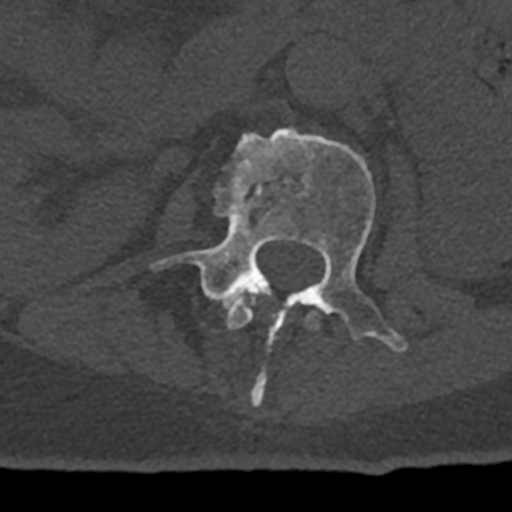
CT including the spine, one axial slice; slice 388 of 797 in the series (ordered by position); bone window (W 1800 / L 400 HU); 512 × 512 image matrix. Male patient, age 74 years. Case-level facts recorded for this patient, not image findings: primary cancer: renal; vertebrae with lytic lesions (as recorded): T10, L1, L2, L3, L4, L5.
Annotated regions visible in this slice (semi-automatically segmented with operator editing):
- L1 vertebra: box from (x=226, y=290) to (x=319, y=330) px
- L2 vertebra: (x=150, y=128)–(x=408, y=407)